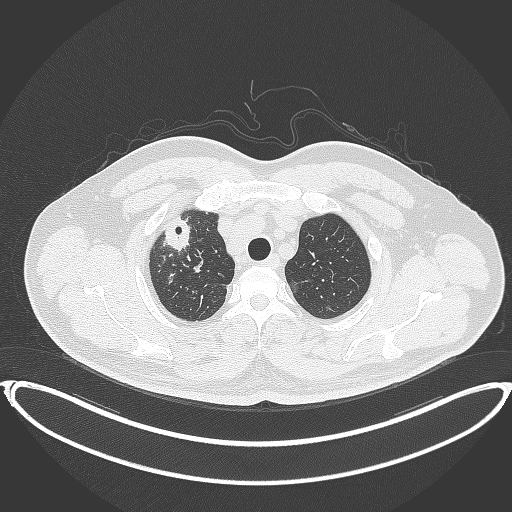
Chest CT, one axial slice. Position 332 of 399 along the scan axis. 120 kVp. Lung window (W 1500 / L -600 HU). 1 mm slice thickness. 512 × 512 image matrix, field of view 445 × 445 mm. Patient: male, 53 years. From the clinical record (not read from this slice): clinical TNM (as recorded): T2a N0 M0.
Annotated regions visible in this slice (bounding box drawn by a radiologist):
- lung tumour (recorded histology: adenocarcinoma): bounding box [x1, y1, x2, y2] px = [162, 216, 200, 253]